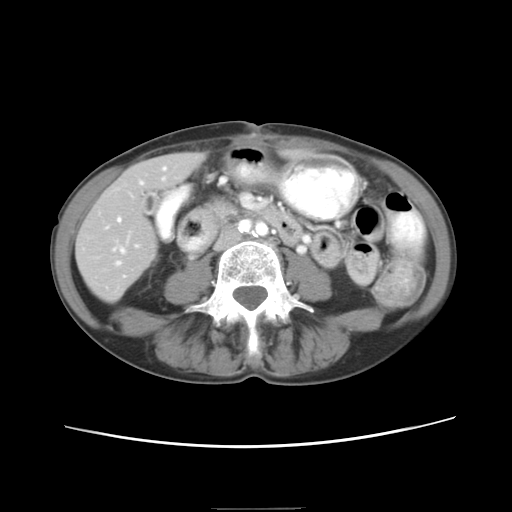
Contrast-enhanced abdominal CT, one axial slice. Position 3 of 26 along the scan axis. Intravenous contrast given. Soft-tissue window (W 400 / L 40 HU). 7.5 mm slice thickness. 512 × 512 image matrix, field of view 340 × 340 mm. Female patient, age 65 years. Case-level facts recorded for this patient, not image findings: diagnosis: colorectal cancer liver metastases, imaged before liver resection; multiple liver metastases: no.
Annotated regions visible in this slice (outlined manually by an expert reader):
- hepatic veins: bounding box (x1, y1, x2, y2) in pixels: (106, 167, 166, 265)
- liver: (78, 153, 198, 300)
- planned liver remnant (the part of the liver to remain after resection): (78, 153, 197, 300)
- portal vein (with intrahepatic branches): (113, 245, 138, 250)